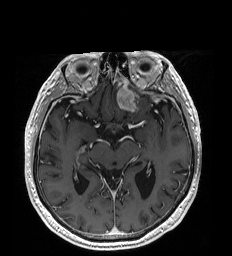
Brain MRI from a brain-tumour surgery series, one axial slice; position 113 of 192 along the scan axis; T1-weighted post-contrast; 1 mm slice thickness; 232 × 256 image matrix. From the clinical record (not read from this slice): histopathology: Glioblastoma; WHO grade: 4; IDH mutation: no.
Structures marked on this image (outlined manually by an expert reader):
- tumour: bounding box [x1, y1, x2, y2] px = [117, 88, 136, 111]